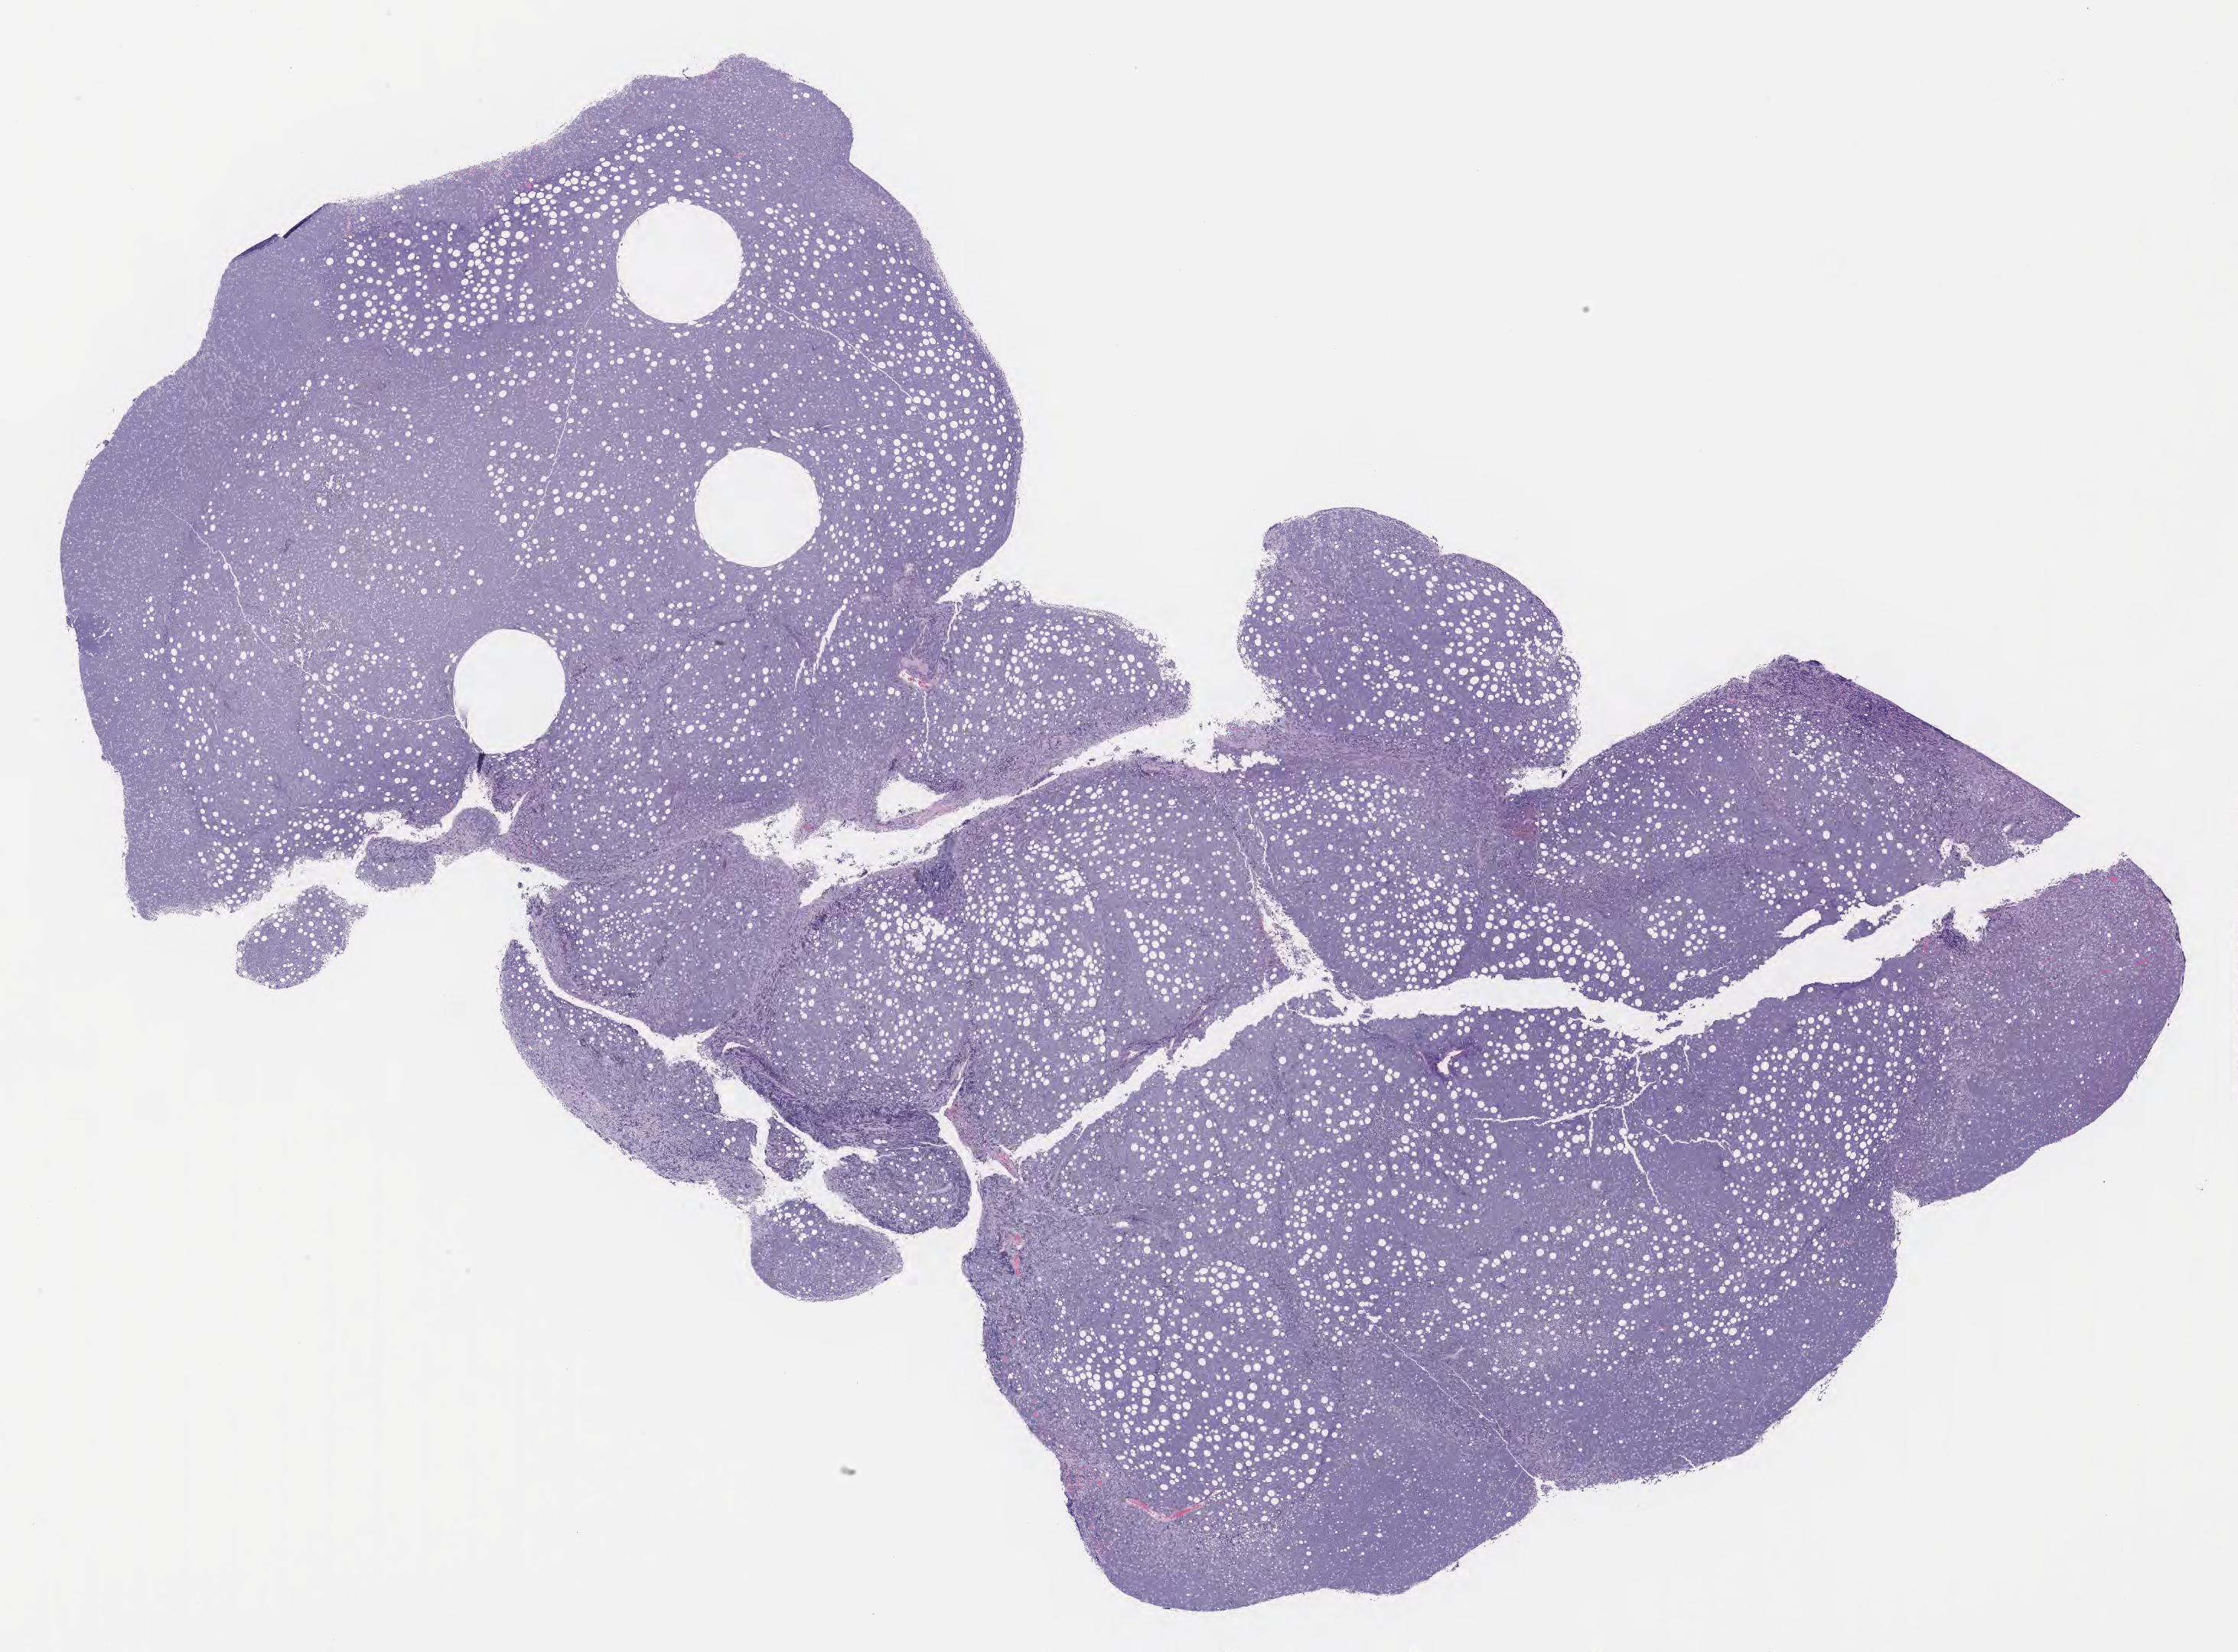
Haematoxylin and eosin whole-slide image, a low-resolution overview of the entire scanned area, about 23.6 x 17.5 mm. Tumor tissue. Site: peritoneum. Patient female; 60 years old.
Diagnosis: Burkitt lymphoma, NOS.